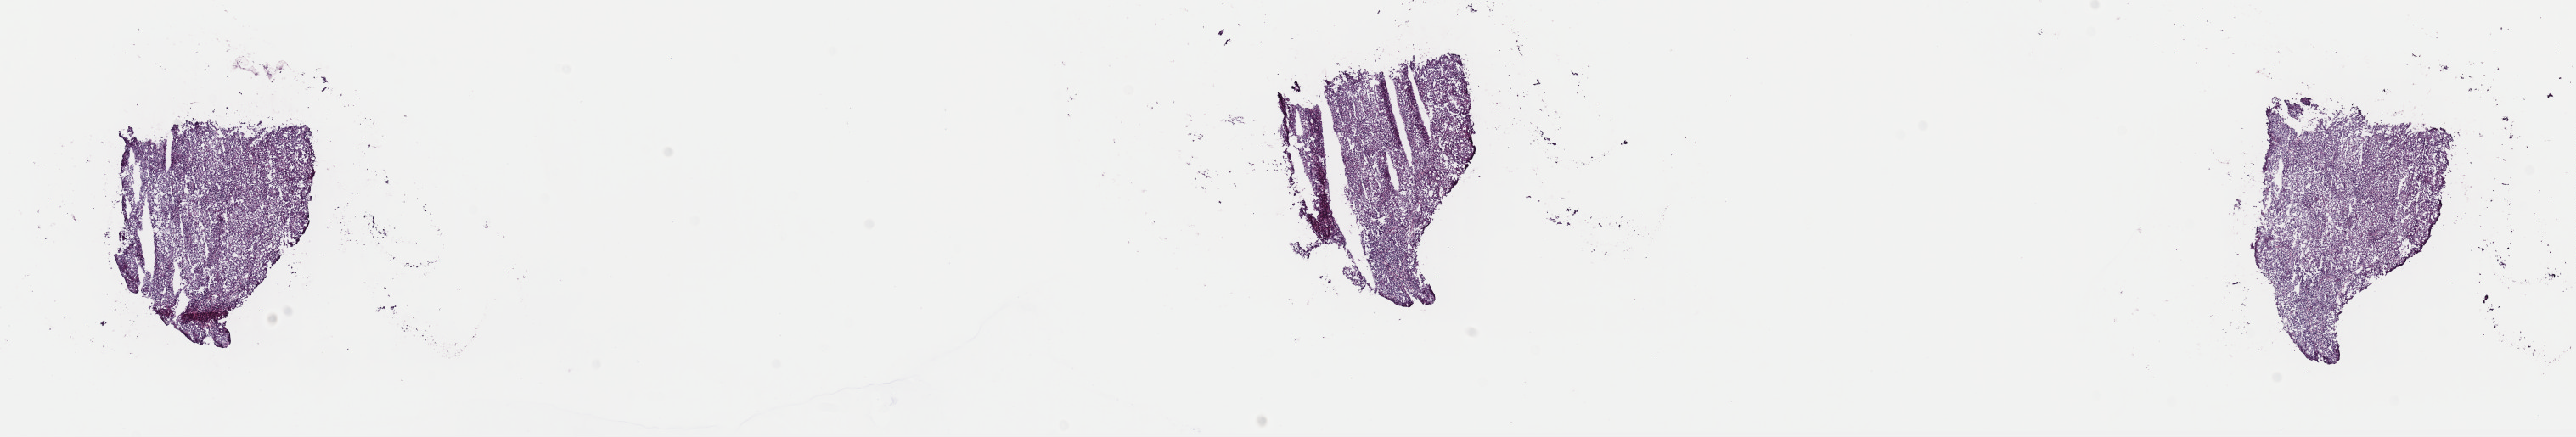
Hematoxylin and eosin (H&E) stained whole-slide image — a low-resolution overview of the entire scanned area, about 24.0 x 4.1 mm (from a 40x scan), frozen section from the top of the tissue portion, kidney, primary tumour sample. Male, age 50 years at initial diagnosis. Histologic grade: G3 (poorly differentiated). Slide review estimates, as recorded: tumour cells 100%, tumour nuclei 95%, normal cells 0%, stromal cells 0%, necrosis 0%. Infiltration values recorded for this section: lymphocyte infiltration 0%, monocyte infiltration 0%, neutrophil infiltration 0%.
• diagnosis: Renal cell carcinoma, NOS
• AJCC pathologic stage: I